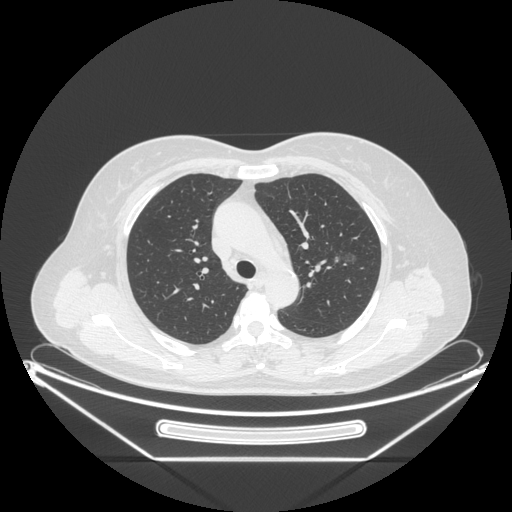
Chest CT, one axial slice. Position 151 of 226 along the scan axis. Reconstruction kernel STANDARD. Lung window (W 1500 / L -600 HU). 512 × 512 image matrix. Patient: female, 54 years. From the clinical record (not read from this slice): clinical TNM (as recorded): T1c N0 M0.
Outlined on this slice (bounding box drawn by a radiologist):
- lung tumour (recorded histology: adenocarcinoma): bounding box [x1, y1, x2, y2] px = [329, 241, 357, 271]